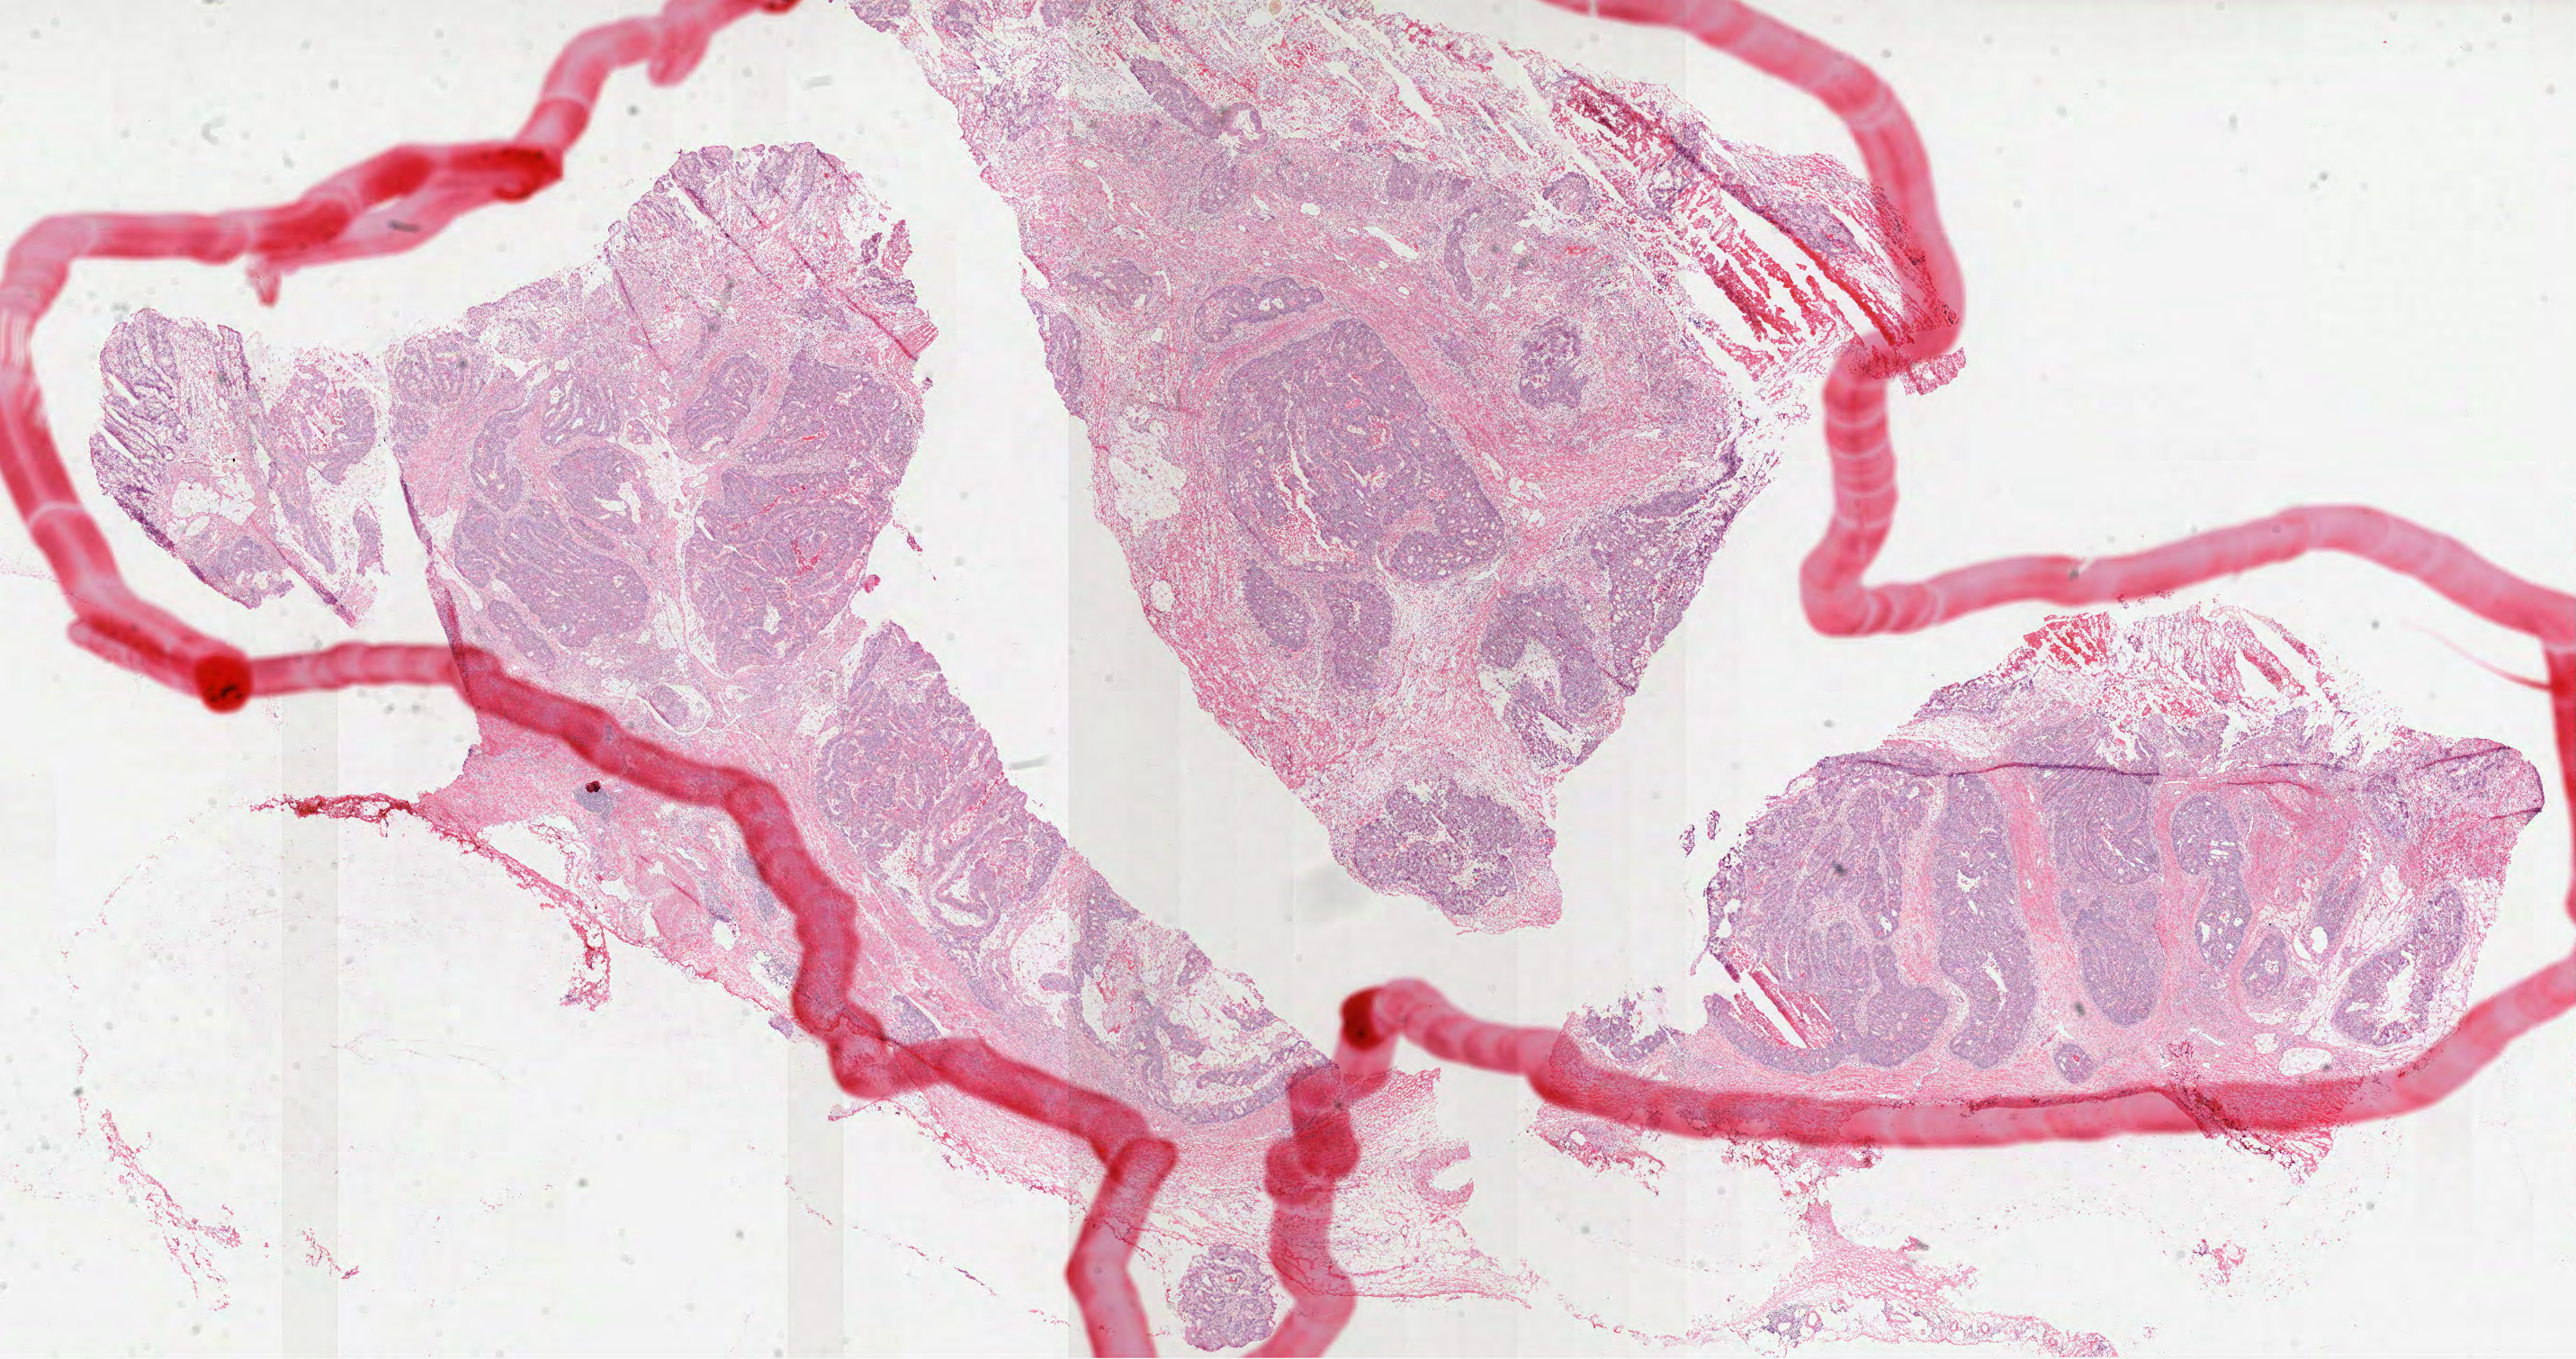
Digitized H&E tissue section (whole slide) — whole scanned area (about 23.1 x 12.2 mm) shown as a low-resolution overview. Frozen section. Sample: primary tumour, colon. Male patient; age at initial diagnosis 51 years. Slide review estimates, as recorded: tumour cells 95%, tumour nuclei 80%, normal cells 0%, stromal cells 0%, necrosis 5%. Infiltration values recorded for this section: lymphocyte infiltration 2%, monocyte infiltration 0%, neutrophil infiltration 1%.
AJCC pathologic stage: IIA (7th edition). Lymph nodes positive (case pathology): 0 of 18 examined. Histologic diagnosis: Mucinous adenocarcinoma.